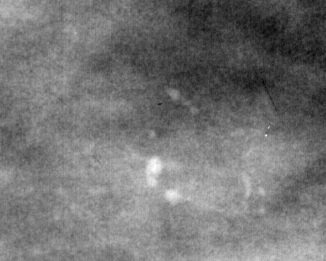
Cropped region of a digitized screen-film mammogram centred on a radiologist-marked abnormality; right breast; CC view; BI-RADS breast density category 3 (scale 1–4).
Marked abnormality: calcifications, morphology pleomorphic, distribution linear; BI-RADS assessment category 4; pathology (as recorded): malignant.